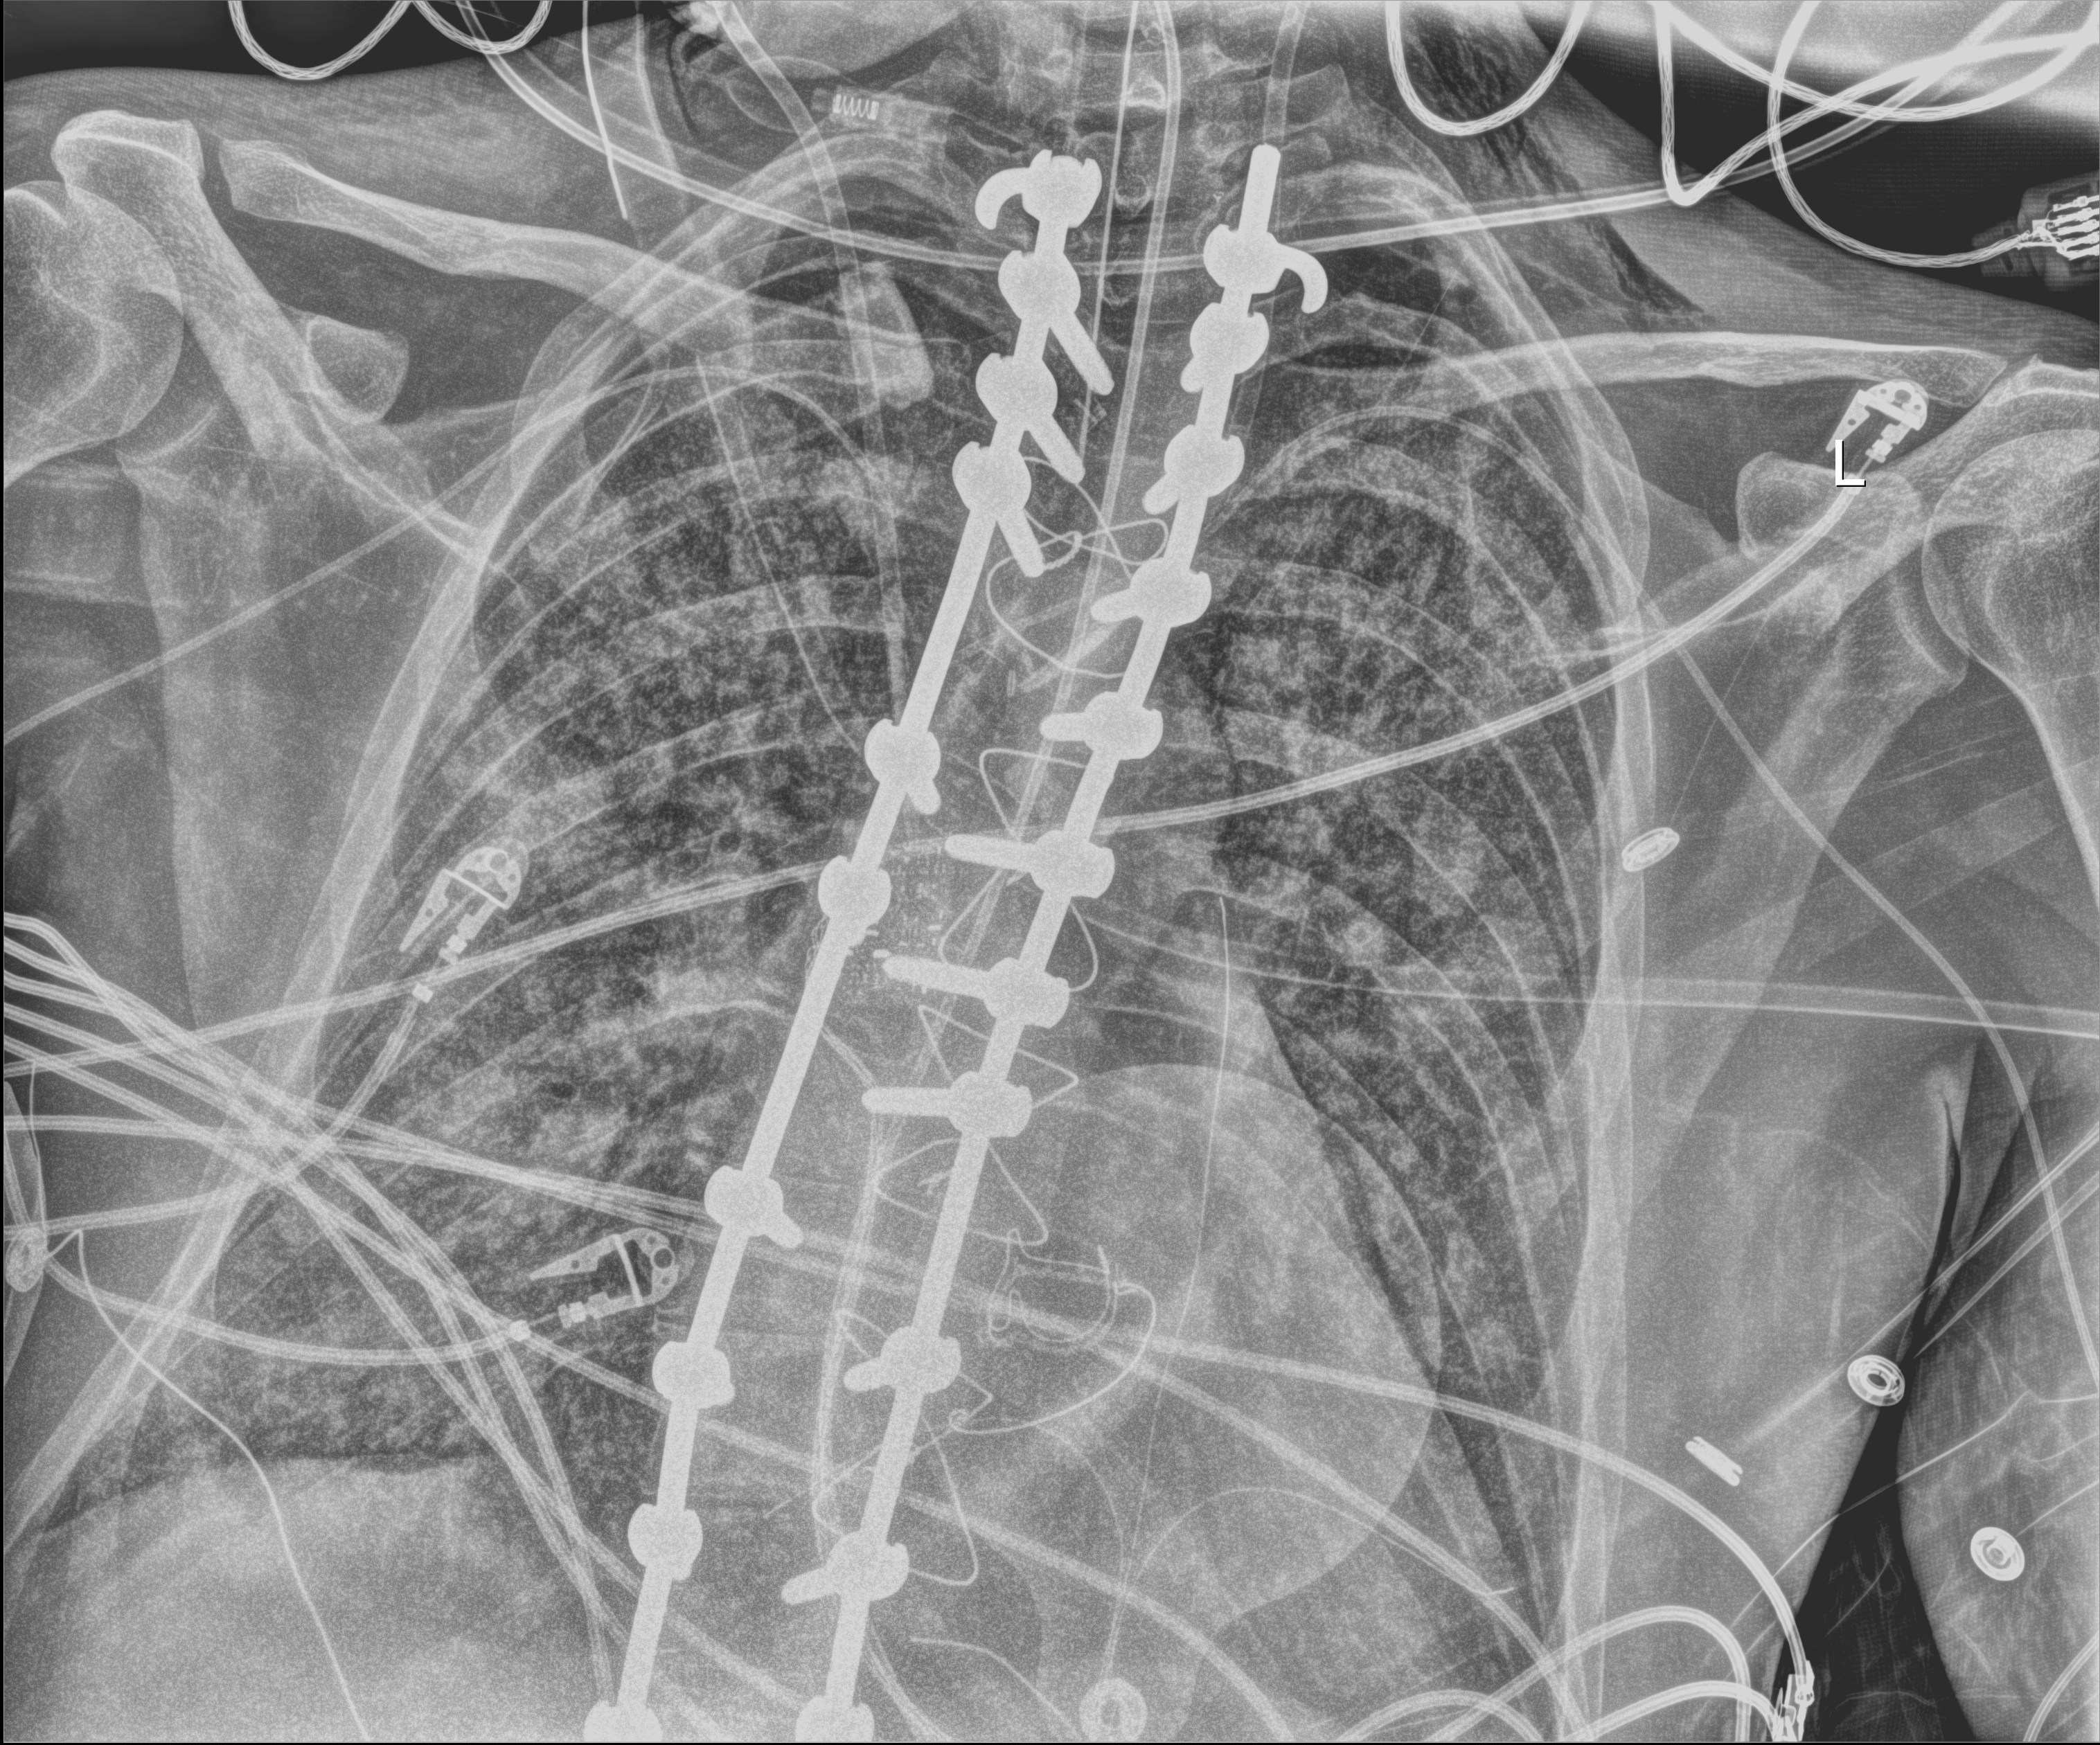
Portable chest radiograph, anteroposterior (AP) projection. Adult patient hospitalised with COVID-19, age 18–59 years.
Hospital-stay facts (about this admission, not read from this image; timing relative to this image not recorded): mechanically ventilated during this hospital stay: yes; length of hospital stay: 15 days; admitted to intensive care during this hospital stay: yes.